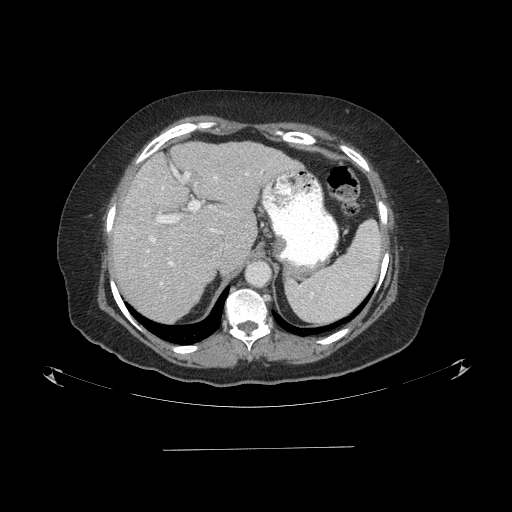
Contrast-enhanced abdominal CT (liver protocol), one axial slice; slice 62 of 103 in the series (ordered by position); 120 kVp; one of 2 acquisitions stored at this slice position; soft-tissue window (W 400 / L 40 HU); 2.5 mm slice thickness; 512 × 512 image matrix, field of view 500 × 500 mm. From the clinical record (not read from this slice): diagnosis: hepatocellular carcinoma (patient treated with transarterial chemoembolisation; whether this scan precedes or follows treatment is not stated here); TNM stage (as recorded): Stage-IIIA; Child-Pugh class: A; tumour differentiation: poorly differentiated; tumour size: 5.2 cm.
Annotated regions visible in this slice (semi-automatically segmented with operator editing):
- abdominal aorta: box from (x=247, y=262) to (x=270, y=285) px
- liver parenchyma outside the tumour (the mass and vessels are separate outlines, so this box may not span the whole liver): (x=110, y=142)–(x=298, y=322)
- liver vessels: (x=145, y=168)–(x=262, y=285)